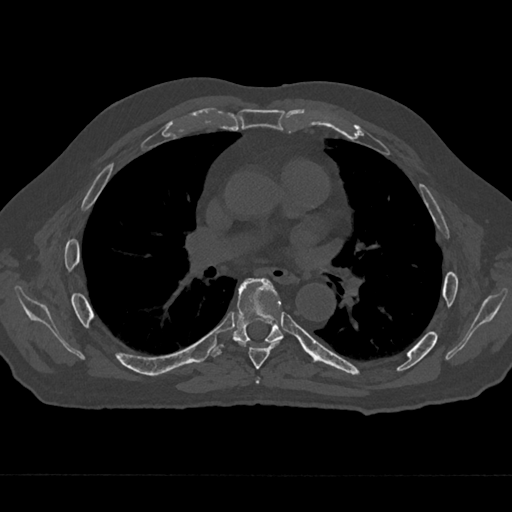
CT including the spine, one axial slice; position 397 of 797 along the scan axis; bone window (W 1800 / L 400 HU); 0.5 mm slice thickness; 512 × 512 image matrix, field of view 377 × 377 mm. Patient: male, 75 years. Case-level facts recorded for this patient, not image findings: primary cancer: renal; vertebrae with lytic lesions (as recorded): T4.
Annotated regions visible in this slice (semi-automatic segmentation, software-assisted and operator-edited):
- T5 vertebra: bounding box [x1, y1, x2, y2] px = [255, 378, 260, 384]
- T6 vertebra: [238, 341, 280, 369]
- T7 vertebra: [210, 278, 284, 357]